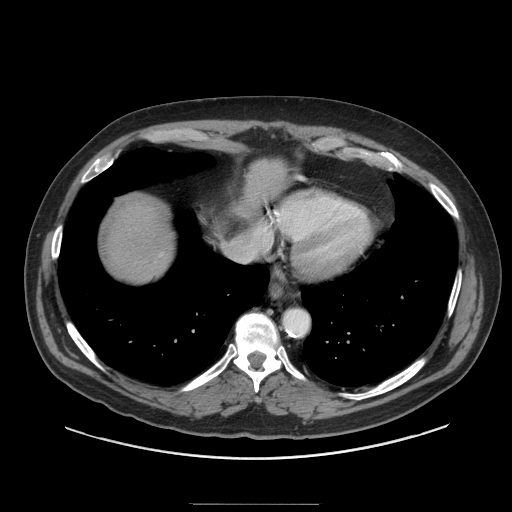
Contrast-enhanced abdominal CT (liver protocol), one axial slice. Position 84 of 91 along the scan axis. Reconstruction kernel STANDARD. Soft-tissue window (W 400 / L 40 HU). 2.5 mm slice thickness. 512 × 512 image matrix, field of view 440 × 440 mm. Case-level facts recorded for this patient, not image findings: diagnosis: hepatocellular carcinoma (patient treated with transarterial chemoembolisation; whether this scan precedes or follows treatment is not stated here); TNM stage (as recorded): Stage-I; Child-Pugh class: A.
Outlined on this slice (semi-automatic segmentation, software-assisted and operator-edited):
- liver parenchyma outside the tumour (the mass and vessels are separate outlines, so this box may not span the whole liver): box from (x=104, y=194) to (x=174, y=282) px